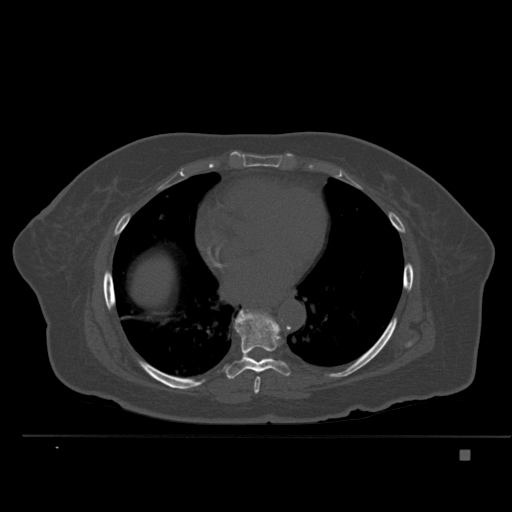
CT including the spine, one axial slice; position 312 of 477 along the scan axis; bone window (W 1800 / L 400 HU); 1.5 mm slice thickness; 512 × 512 image matrix, field of view 422 × 422 mm. Female patient, age 74 years. From the clinical record (not read from this slice): primary cancer: colon.
Outlined on this slice (semi-automatic segmentation, software-assisted and operator-edited):
- T6 vertebra: bounding box (x1, y1, x2, y2) in pixels: (225, 371, 227, 374)
- T7 vertebra: (254, 377, 261, 394)
- T8 vertebra: (224, 310, 290, 379)
- T9 vertebra: (251, 358, 254, 360)